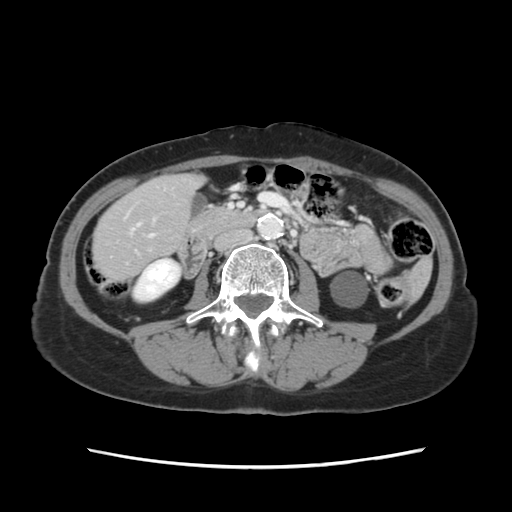
Contrast-enhanced abdominal CT, one axial slice. Position 23 of 120 along the scan axis. 120 kVp. Intravenous contrast given. Soft-tissue window (W 400 / L 40 HU). 2.5 mm slice thickness. 512 × 512 image matrix. Female patient, age 70 years. Case-level facts recorded for this patient, not image findings: diagnosis: colorectal cancer liver metastases, imaged before liver resection; multiple liver metastases: no.
Outlined on this slice (outlined manually by an expert reader):
- hepatic veins: bounding box [x1, y1, x2, y2] px = [149, 235, 153, 237]
- liver: [95, 176, 200, 278]
- planned liver remnant (the part of the liver to remain after resection): [95, 176, 199, 278]
- portal vein (with intrahepatic branches): [131, 224, 140, 231]